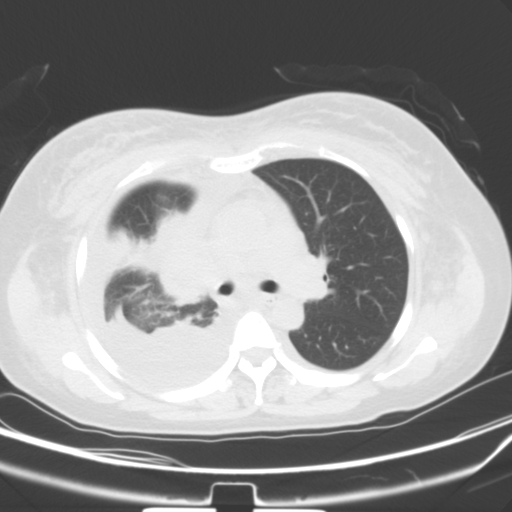
Chest CT, one axial slice. Position 33 of 54 along the scan axis. 120 kVp. Lung window (W 1500 / L -600 HU). 5 mm slice thickness. 512 × 512 image matrix. Female patient, age 36 years. From the clinical record (not read from this slice): clinical TNM (as recorded): T1b N2 M0.
Outlined on this slice (rectangle marked by the reading radiologist):
- lung tumour (recorded histology: adenocarcinoma): bounding box [x1, y1, x2, y2] px = [157, 191, 212, 308]